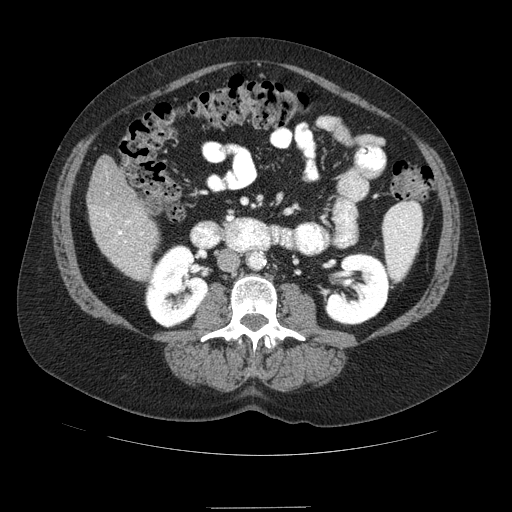
Contrast-enhanced abdominal CT (liver protocol), one axial slice; position 22 of 89 along the scan axis; reconstruction kernel STANDARD; soft-tissue window (W 400 / L 40 HU); 512 × 512 image matrix. Case-level facts recorded for this patient, not image findings: diagnosis: hepatocellular carcinoma (patient treated with transarterial chemoembolisation; whether this scan precedes or follows treatment is not stated here); TNM stage (as recorded): Stage-IIIB; Child-Pugh class: A; tumour nodularity: multinodular.
Outlined on this slice (semi-automatically segmented with operator editing):
- liver parenchyma outside the tumour (the mass and vessels are separate outlines, so this box may not span the whole liver): box from (x=88, y=156) to (x=158, y=279) px
- liver vessels: (x=107, y=214)–(x=143, y=241)